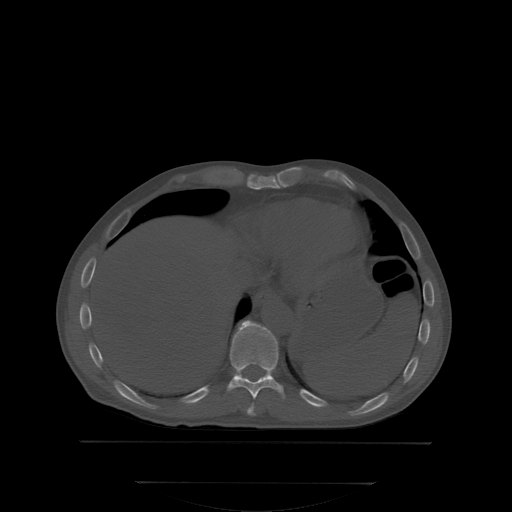
CT including the spine, one axial slice; bone window (W 1800 / L 400 HU); 2.5 mm slice thickness; 512 × 512 image matrix, field of view 500 × 500 mm. Male patient, age 58 years. Case-level facts recorded for this patient, not image findings: primary cancer: prostate.
Annotated regions visible in this slice (semi-automatic segmentation, software-assisted and operator-edited):
- T10 vertebra: bounding box (x1, y1, x2, y2) in pixels: (228, 322, 283, 398)
- T9 vertebra: (248, 404, 255, 414)